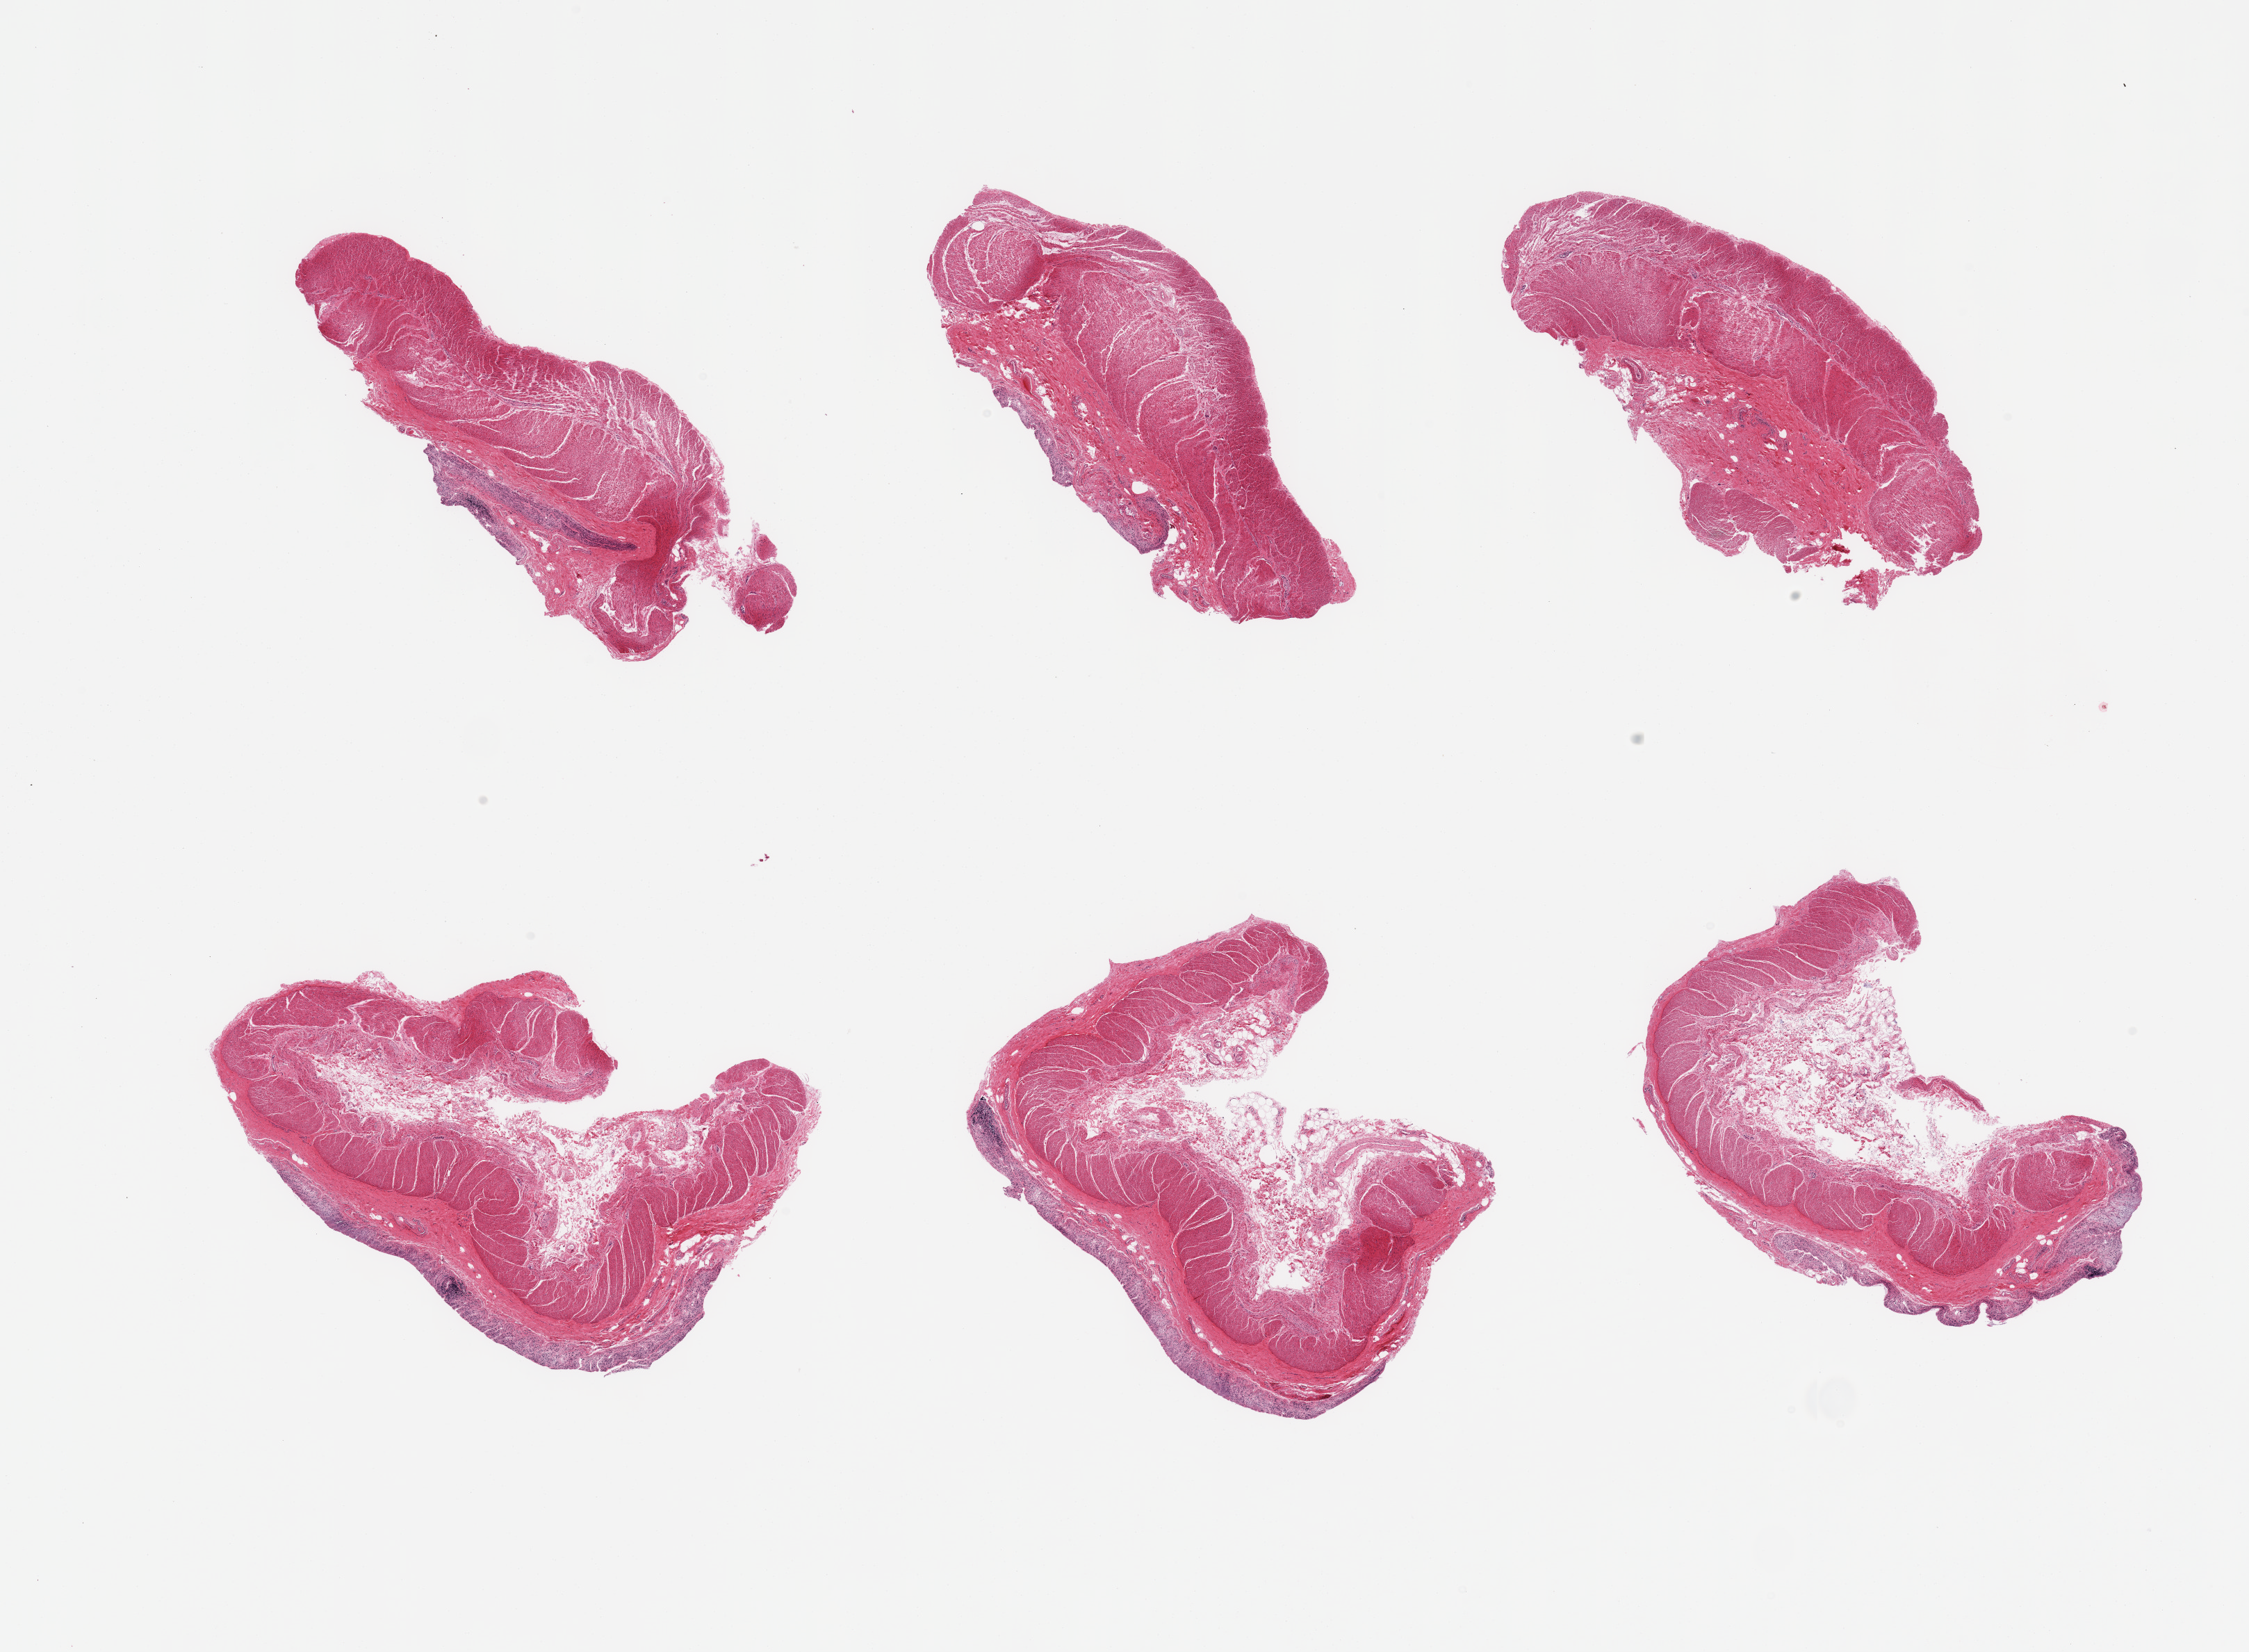
Digitized haematoxylin and eosin-stained section, shown as a low-resolution overview of the whole scanned area (about 25.6 x 18.8 mm, slide scanned at 20x), PAXgene-fixed, paraffin-embedded tissue, target tissue: sigmoid colon, tissue donor sample. Donor sex: male.
• reviewer comment on this tissue sample: 6 pieces, target muscularis is ~90% of tissue, rest is autolyzed mucosa